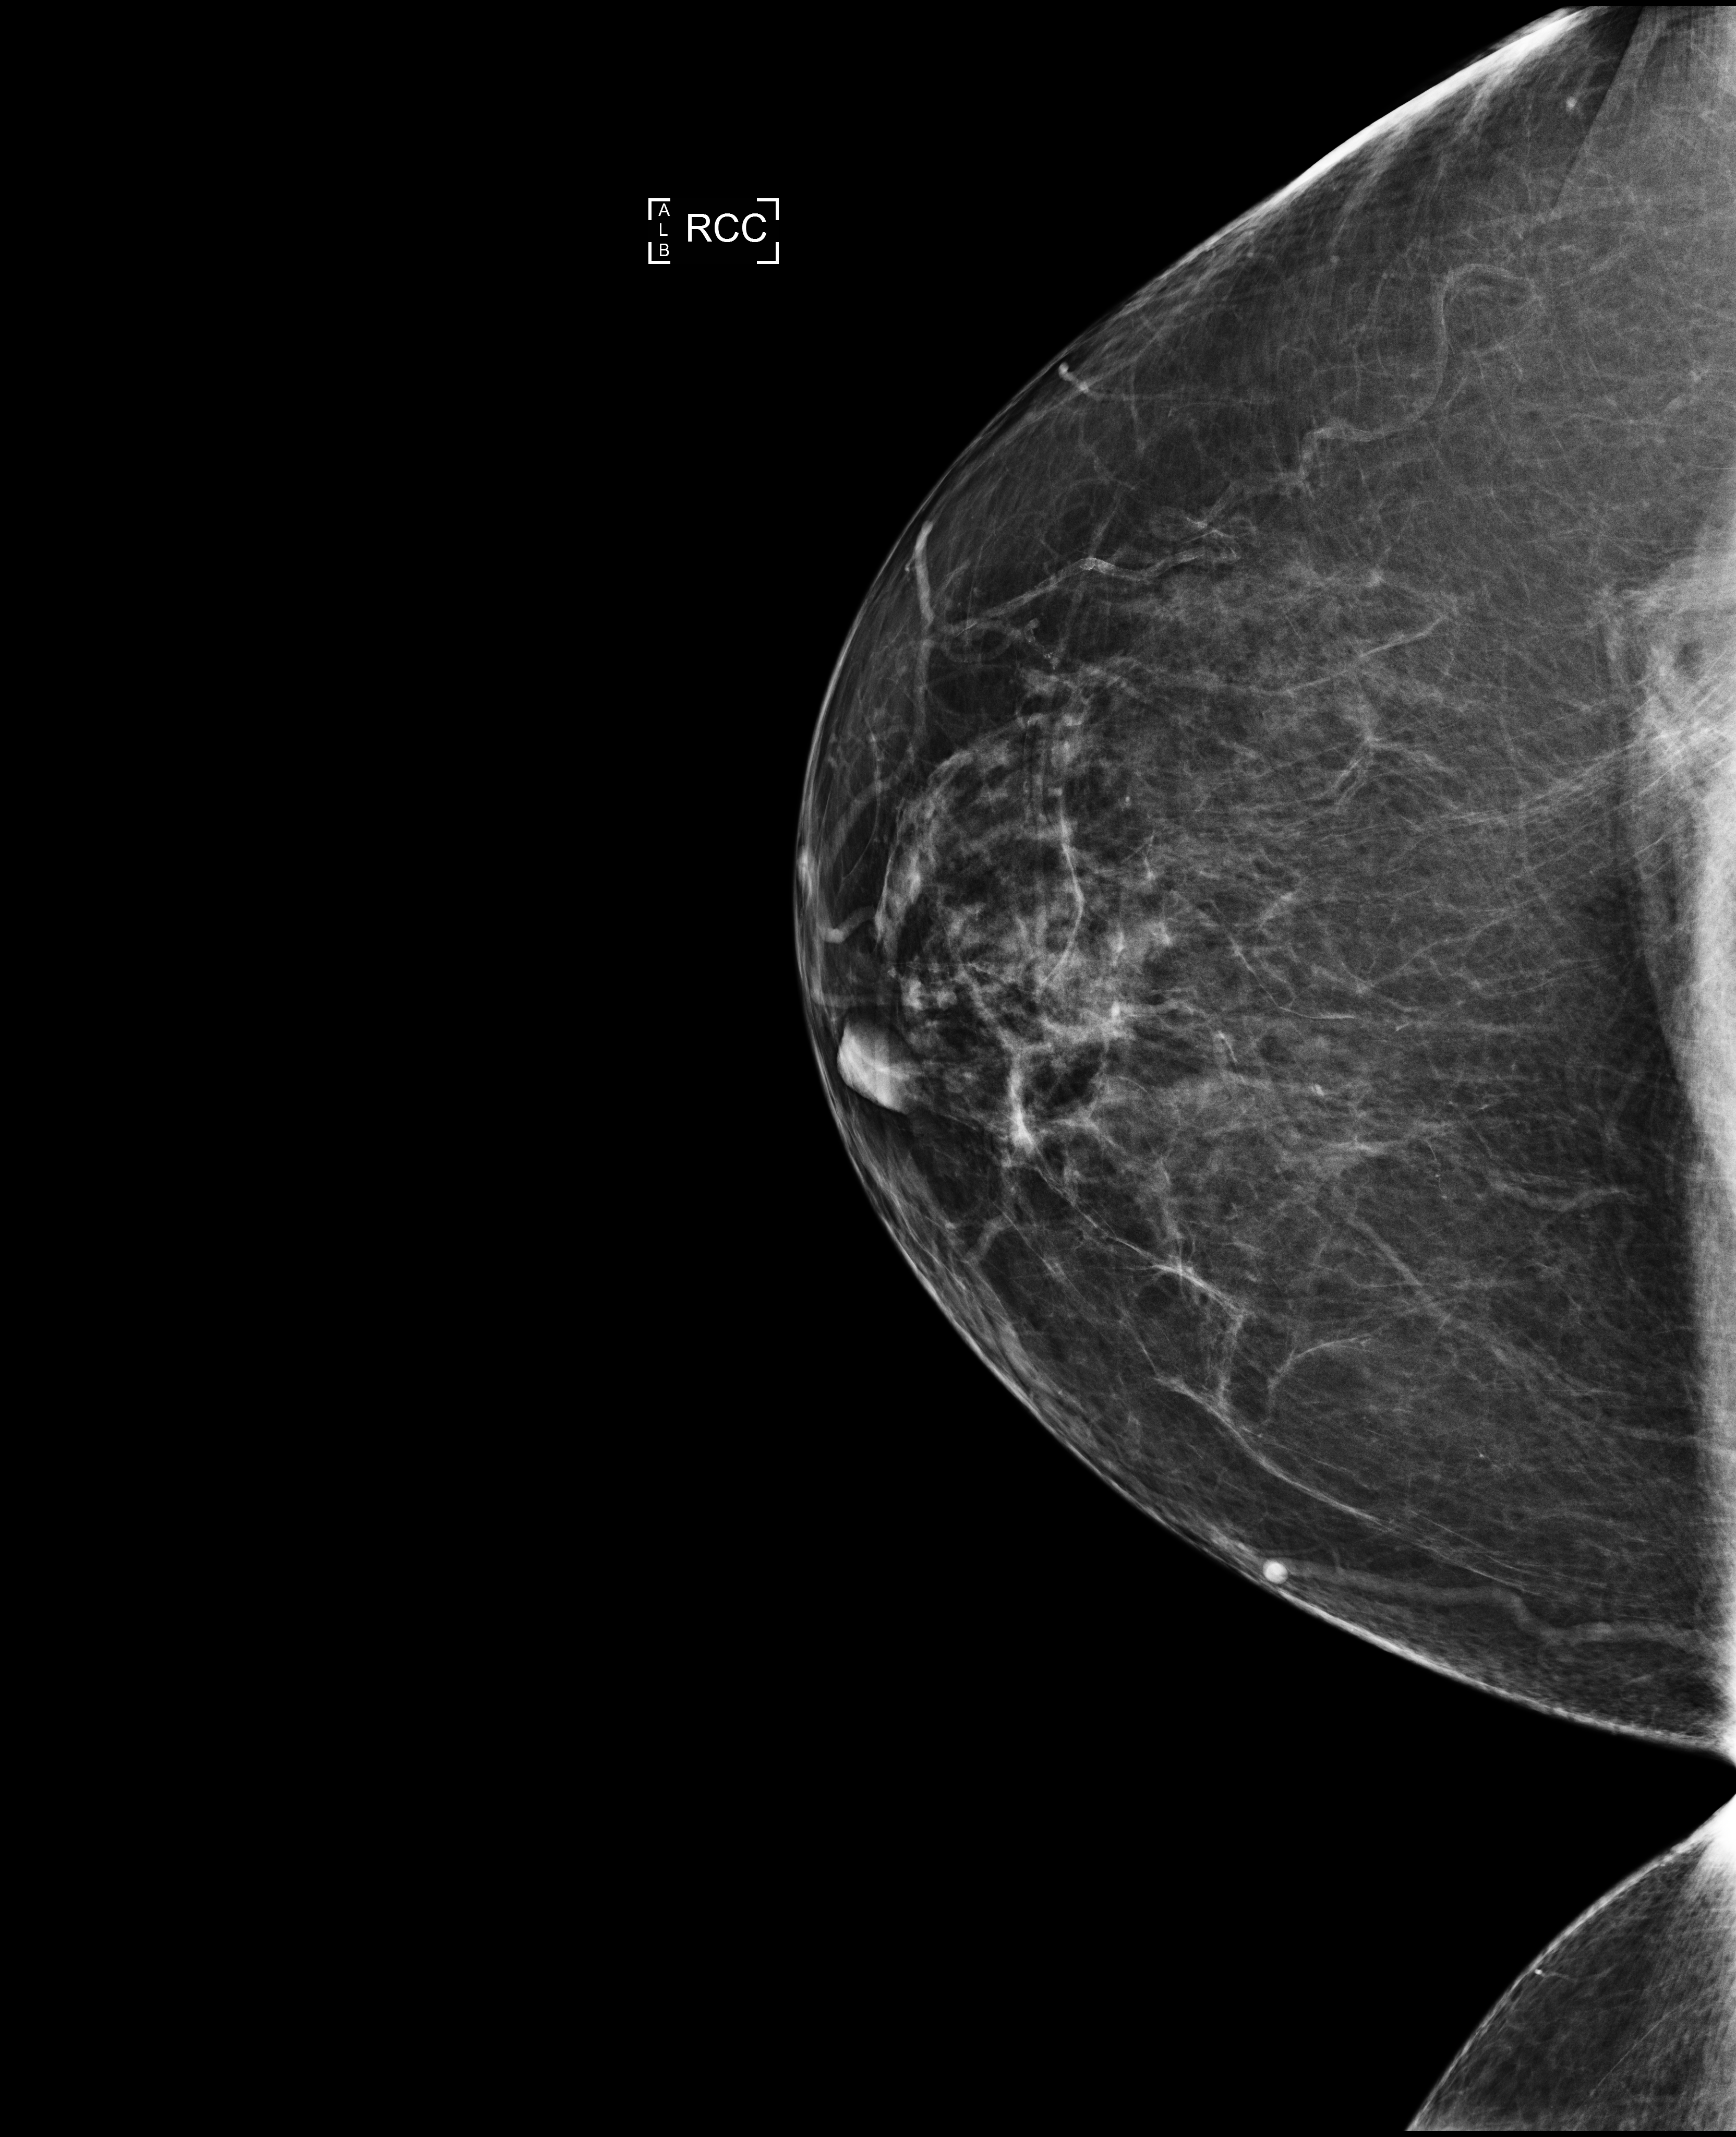
Annual screening mammography examination, compressed breast thickness 79 mm, system: Selenia Dimensions. Female patient, age 62 years.
Image type: full-field digital mammogram. Breast: right. Projection: cranio-caudal projection.